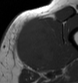
MRI of an extremity soft-tissue mass, one axial slice; position 20 of 43 along the scan axis; MR volume resampled by the dataset authors to the PET/CT grid (not the native acquisition matrix); 3.27 mm slice thickness; 78 × 83 image matrix, field of view 76 × 81 mm. Male patient. From the clinical record (not read from this slice): histological type: pleiomorphic leiomyosarcoma; grade: high; site of the primary tumour: left thigh.
Annotated regions visible in this slice (expert contour drawn on MRI and transferred to this co-registered scan by the dataset authors):
- gross tumour volume including surrounding oedema: bounding box <15,17,60,68> (left, top, right, bottom; pixels)
- gross tumour volume (mass): <15,17,55,66>